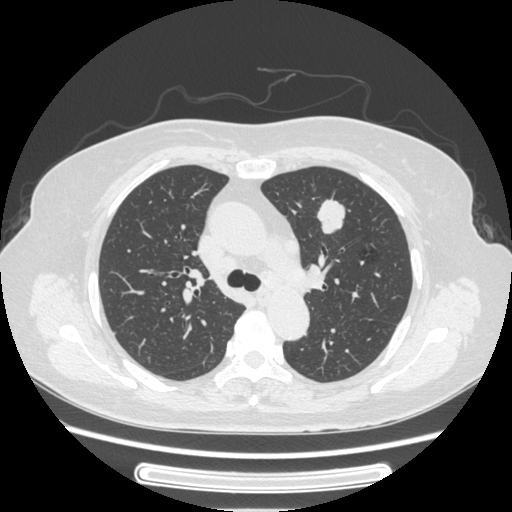
Chest CT, one axial slice. Position 163 of 227 along the scan axis. Lung window (W 1500 / L -600 HU). 1.25 mm slice thickness. 512 × 512 image matrix, field of view 363 × 363 mm. Female patient, age 77 years. Case-level facts recorded for this patient, not image findings: clinical TNM (as recorded): T1c N3 M0; histopathological grade: G2-3.
Structures marked on this image (rectangle marked by the reading radiologist):
- lung tumour (recorded histology: adenocarcinoma): bounding box <313,196,358,243> (left, top, right, bottom; pixels)